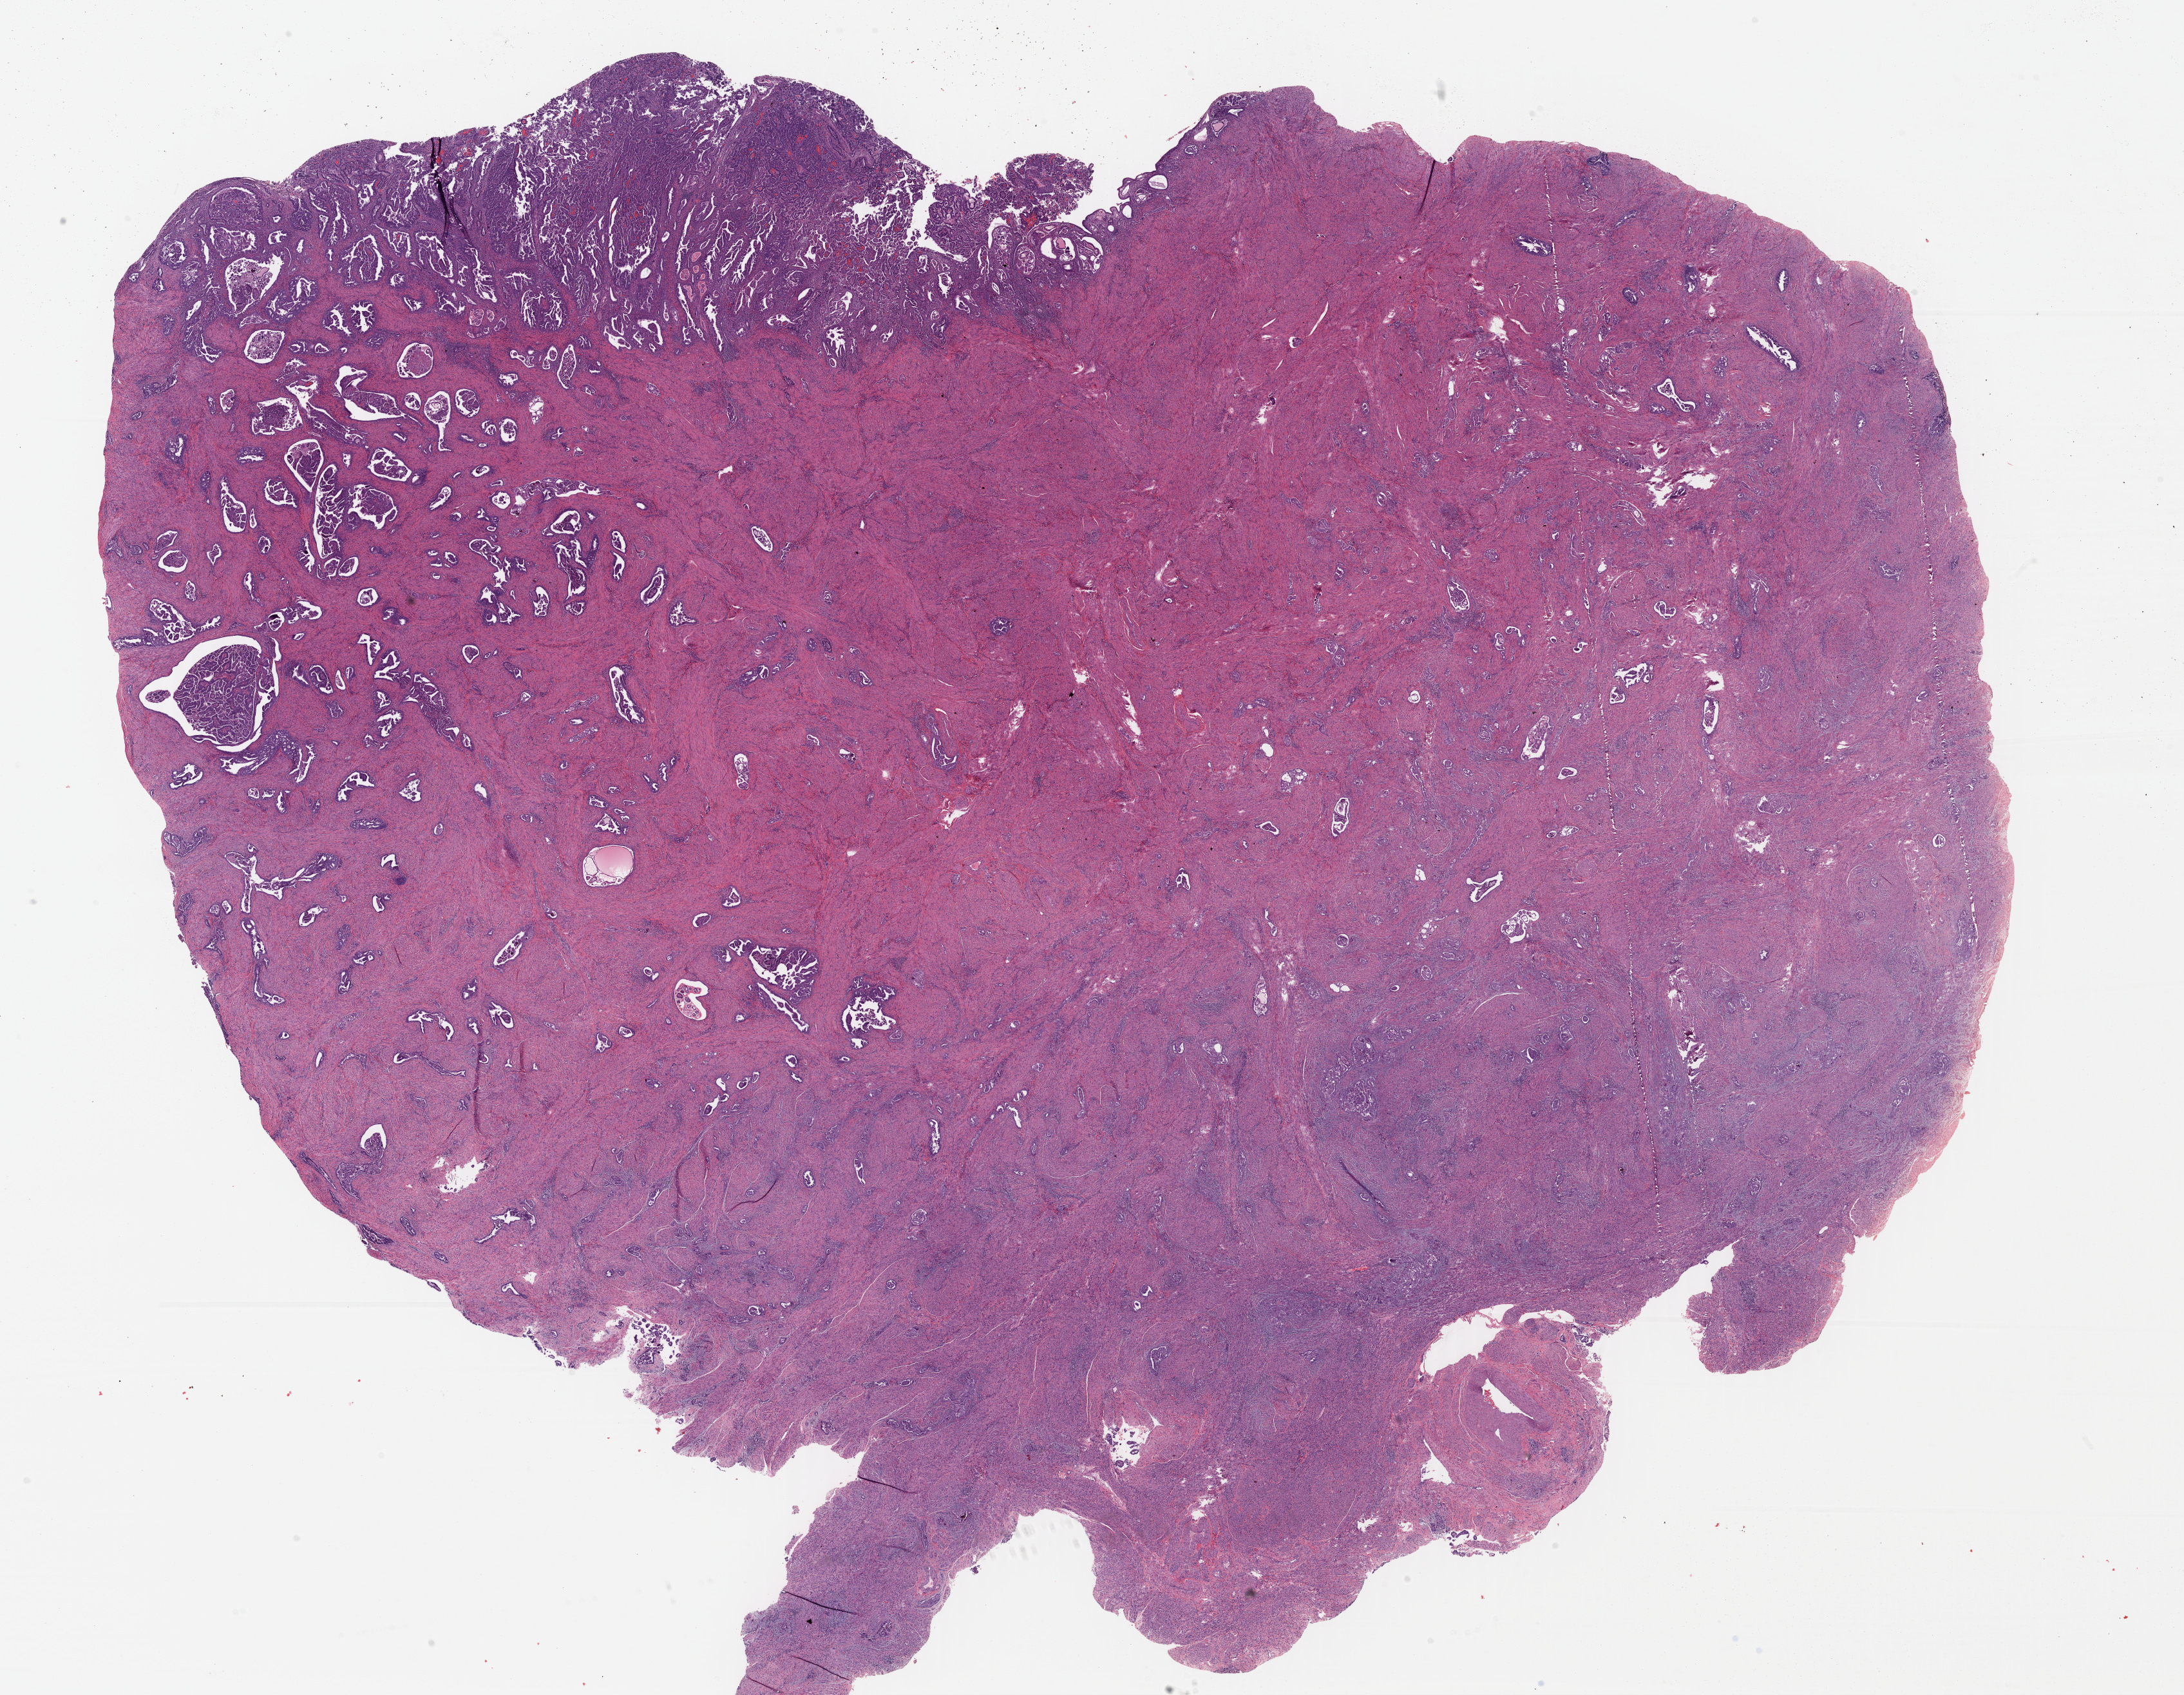
Hematoxylin and eosin (H&E) stained whole-slide image, low-resolution overview of the scanned area, about 26.7 x 20.7 mm; formalin-fixed paraffin-embedded (FFPE) diagnostic section; uterus, primary tumour sample. Patient: female, age at initial diagnosis 51 years. Histologic grade: G3 (poorly differentiated).
• histologic diagnosis: Serous cystadenocarcinoma, NOS (endometrium)
• FIGO stage: IIIC